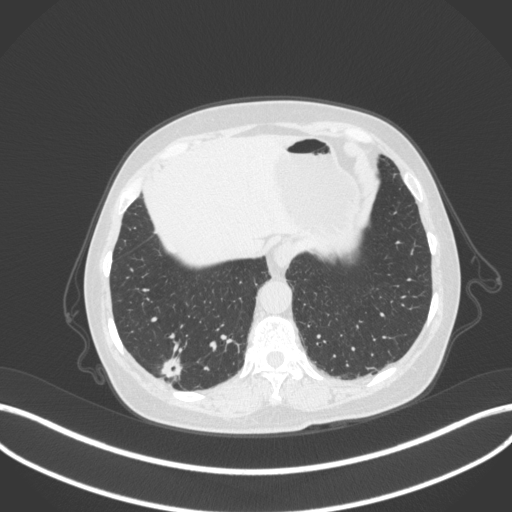
Chest CT, one axial slice; position 56 of 340 along the scan axis; reconstruction kernel B31f; 120 kVp; lung window (W 1500 / L -600 HU); 512 × 512 image matrix, field of view 400 × 400 mm. Female patient, age 69 years. Case-level facts recorded for this patient, not image findings: clinical TNM (as recorded): T1b N0 M0; histopathological grade: G2-3.
Annotated regions visible in this slice (bounding box drawn by a radiologist):
- lung tumour (recorded histology: adenocarcinoma): bounding box <161,352,183,380> (left, top, right, bottom; pixels)